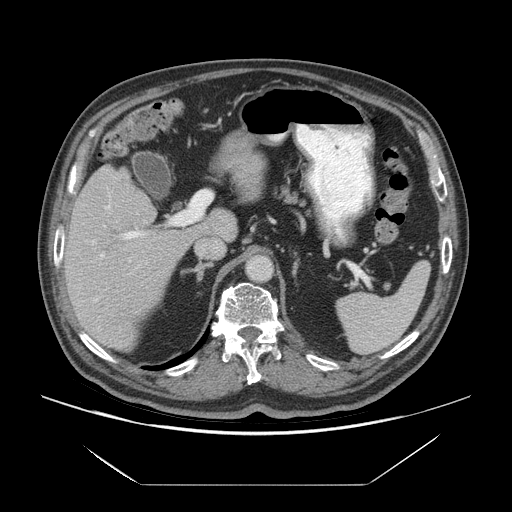
Contrast-enhanced abdominal CT (liver protocol), one axial slice; position 39 of 75 along the scan axis; 140 kVp; soft-tissue window (W 400 / L 40 HU); 2.5 mm slice thickness; 512 × 512 image matrix, field of view 420 × 420 mm. From the clinical record (not read from this slice): diagnosis: hepatocellular carcinoma (patient treated with transarterial chemoembolisation; whether this scan precedes or follows treatment is not stated here); TNM stage (as recorded): Stage-I; Child-Pugh class: A; tumour nodularity: uninodular; tumour size: 5.8 cm.
Annotated regions visible in this slice (semi-automatic segmentation, software-assisted and operator-edited):
- liver parenchyma outside the tumour (the mass and vessels are separate outlines, so this box may not span the whole liver): bounding box <64,164,236,350> (left, top, right, bottom; pixels)
- liver vessels: <92,205,145,302>